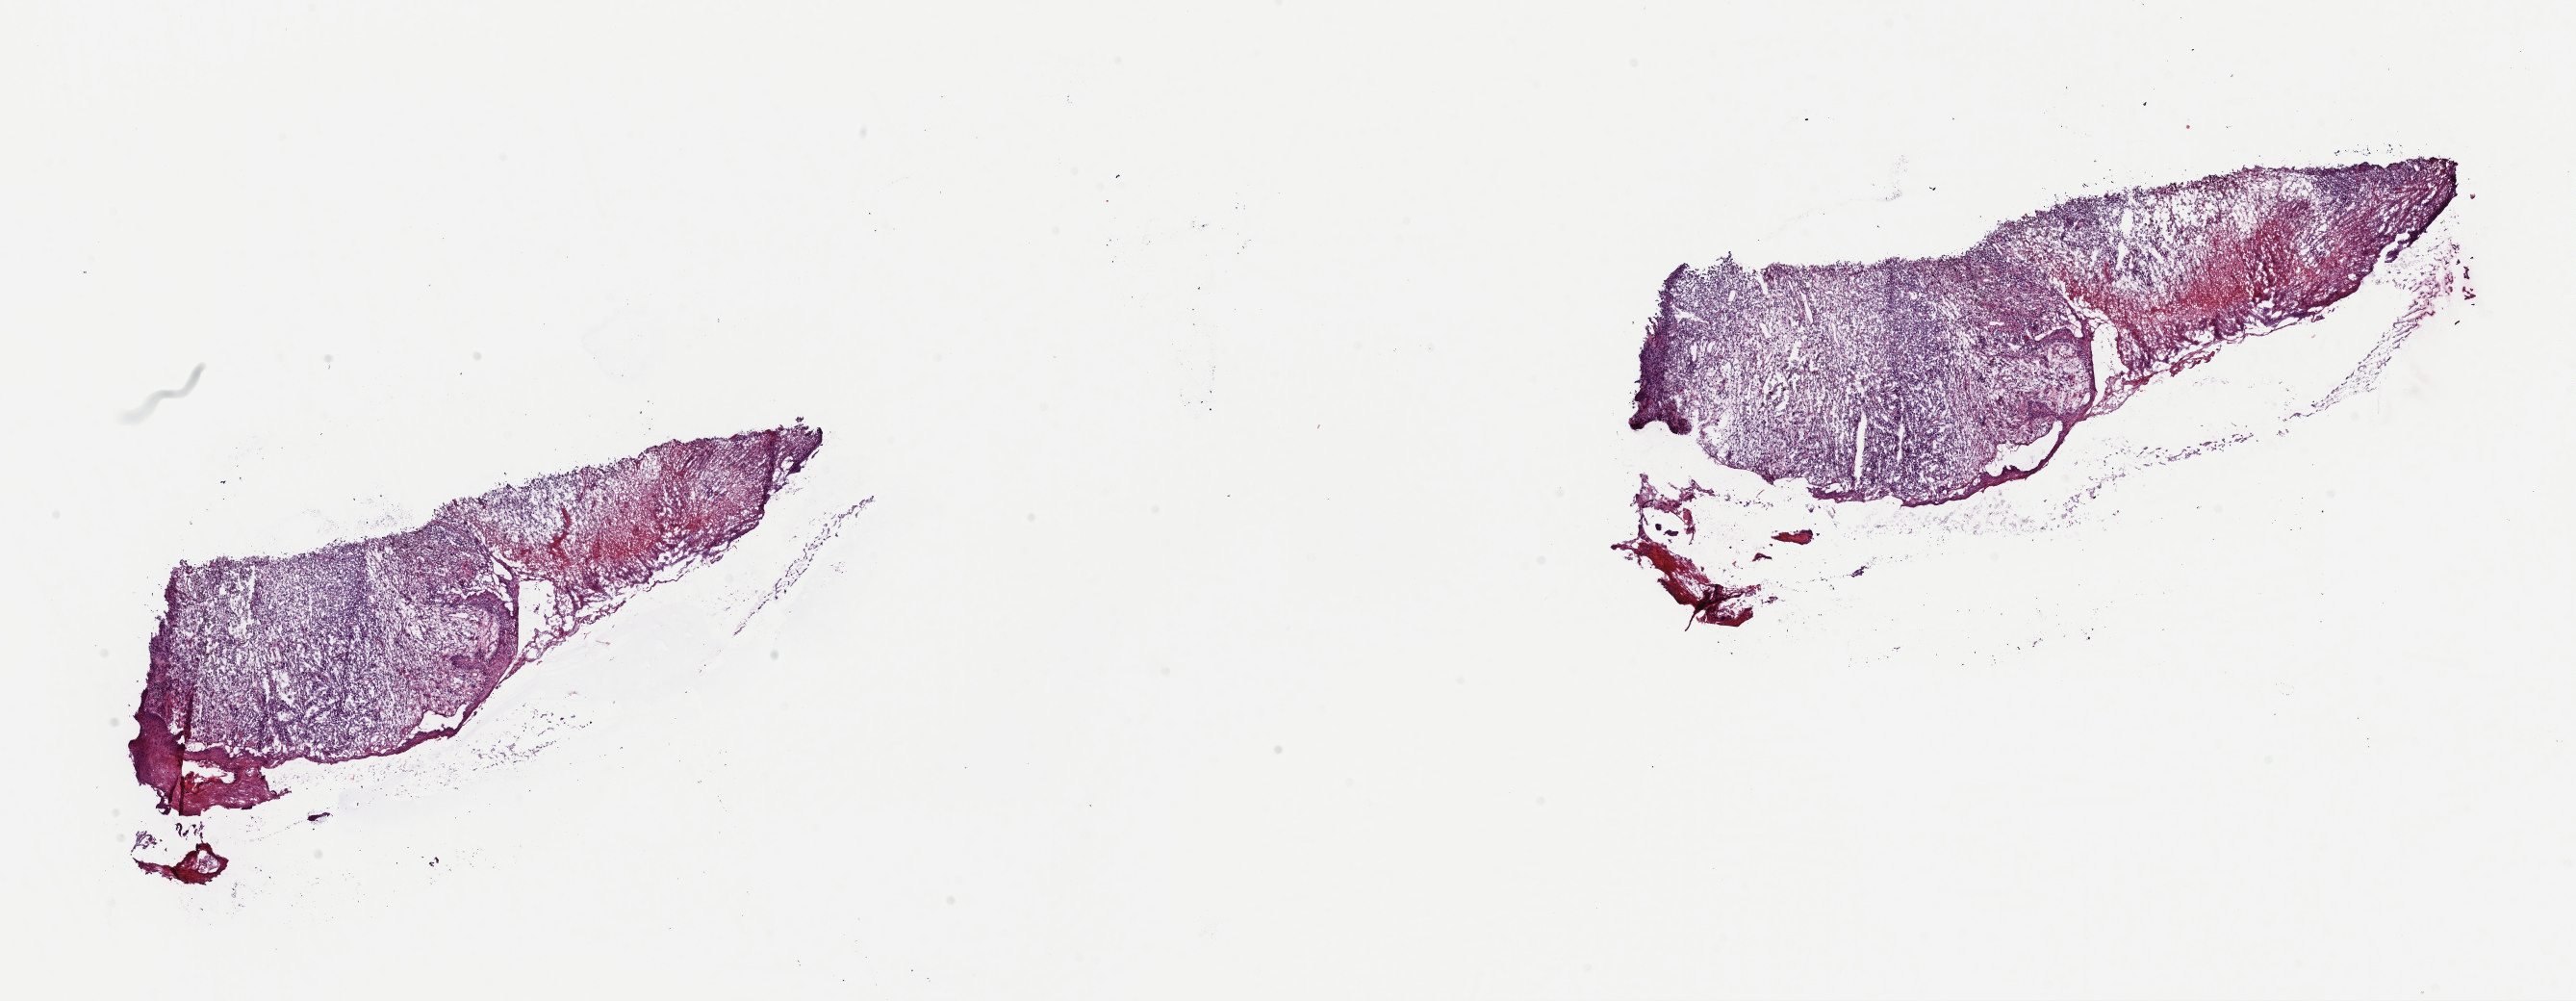
Digitized H&E tissue section (whole slide) — low-resolution overview of the scanned area, about 21.1 x 8.2 mm (slide scanned at 40x); frozen section from the top of the tissue portion; sample: primary tumour, skin. Male patient; age at initial diagnosis 65 years. Pathologist review of this section (percent, as recorded): tumour cells 80%, tumour nuclei 70%, normal cells 15%, stromal cells 5%, necrosis 0%. Inflammatory infiltration, as recorded: lymphocyte infiltration 0%, monocyte infiltration 0%, neutrophil infiltration 0%.
Diagnosis: Malignant melanoma, NOS. AJCC pathologic stage: IIC (7th edition). TNM: T4b N0 M0.